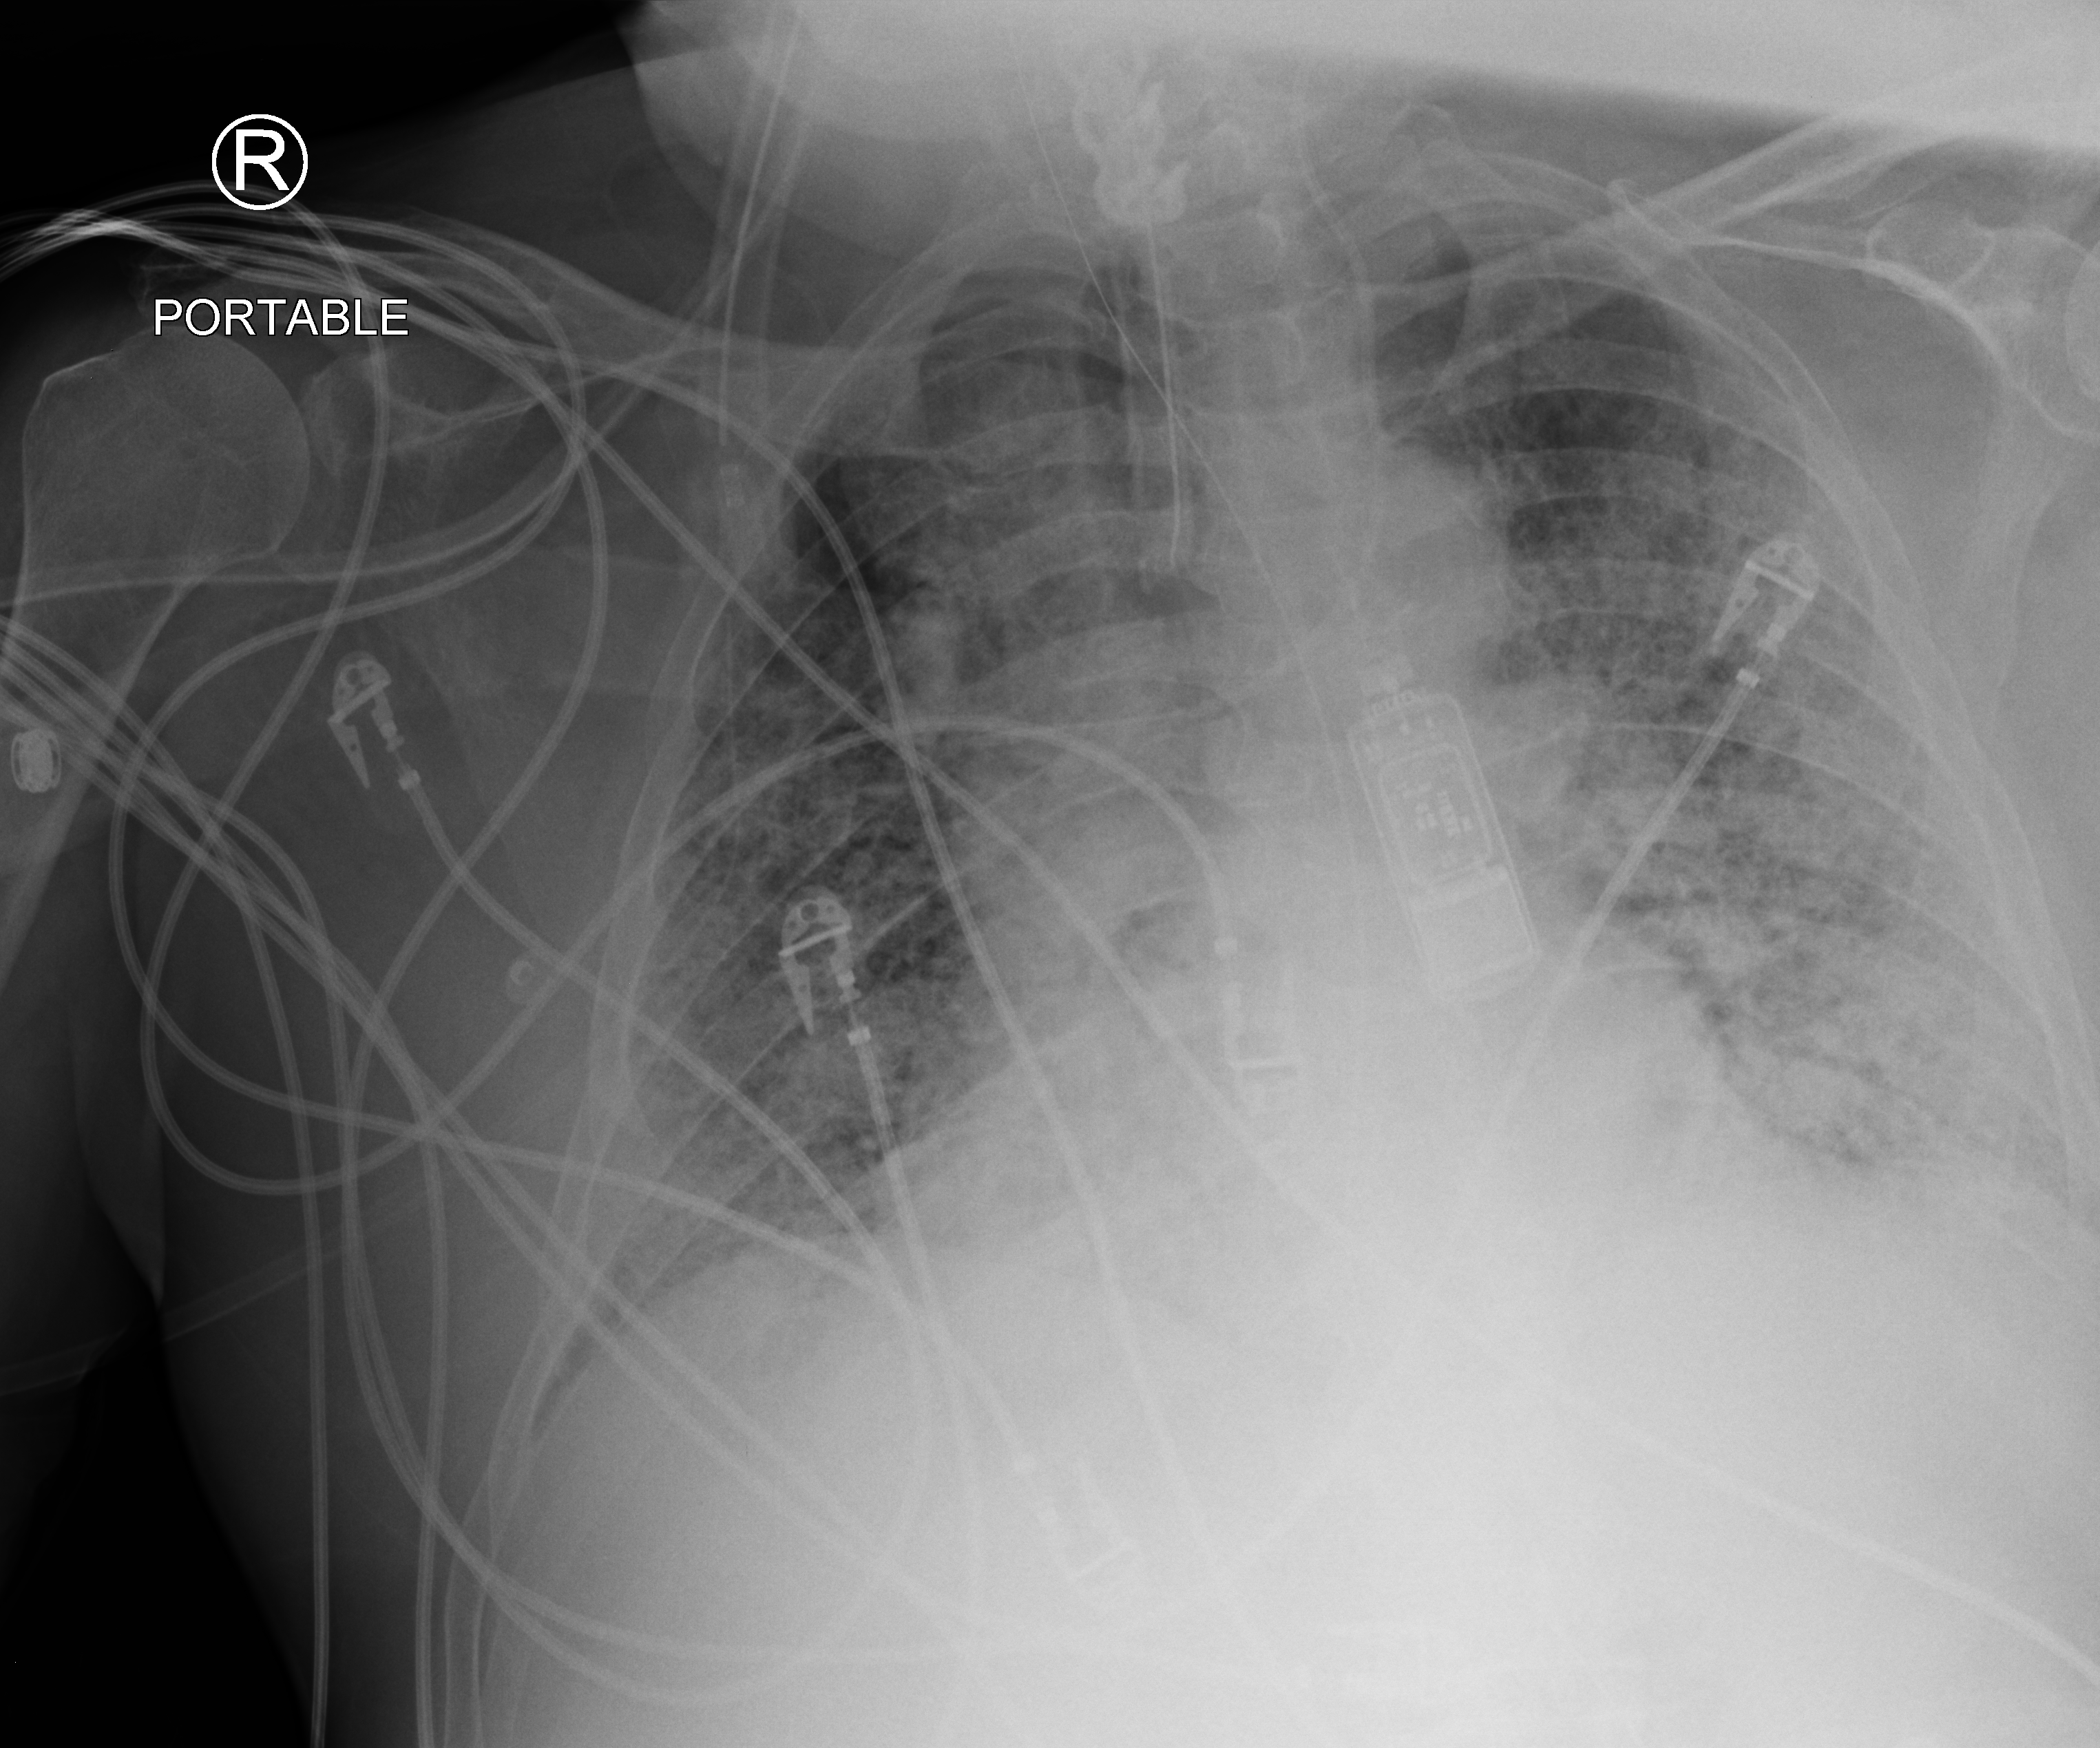
Chest X-ray (portable), anteroposterior (AP) projection. Male patient hospitalised with COVID-19, age 60–74 years.
Admission-level facts for this patient (not findings on this image; timing relative to this image not recorded):
- admitted to intensive care during this hospital stay: yes